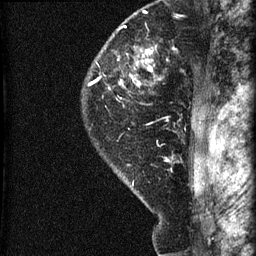
Breast MRI (dynamic contrast-enhanced), one sagittal slice; slice 52 of 60 in the series (ordered by position); dynamic contrast-enhanced series, image 2 of 3 at this slice position (ordered by acquisition); 1.5 T; TE 4.2 ms, TR 22.7 ms; 1.8 mm slice thickness; 256 × 256 image matrix. Patient: female, 45 years. Case-level facts recorded for this patient, not image findings: setting: breast cancer imaged before/during neoadjuvant chemotherapy; receptor status: HR-positive, HER2-negative.
Outlined on this slice (semi-automatically segmented with operator editing):
- analysis volume of interest (the breast-tissue region the enhancement analysis was run in; not a lesion): bounding box <81,11,205,140> (left, top, right, bottom; pixels)
- tumour enhancement mask (voxels above the 90 % enhancement threshold inside the analysis volume of interest): <89,50,153,86>